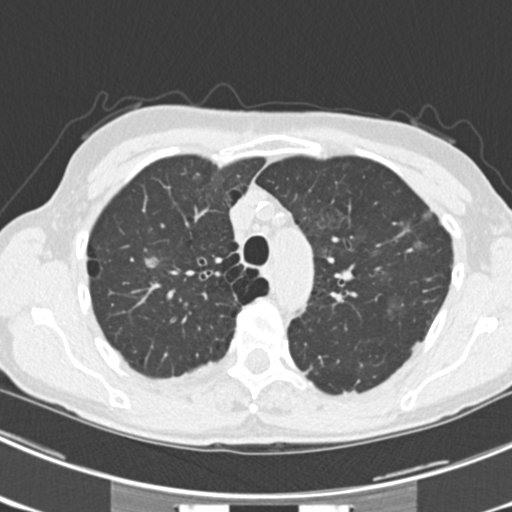
Low-dose screening chest CT, one axial slice; position 168 of 225 along the scan axis; 120 kVp; lung window (W 1500 / L -600 HU); 2 mm slice thickness; 512 × 512 image matrix.
Annotated regions visible in this slice (expert manual segmentation):
- lesion 3 (tumor, upper lobe of right lung): box from (x=143, y=255) to (x=159, y=268) px